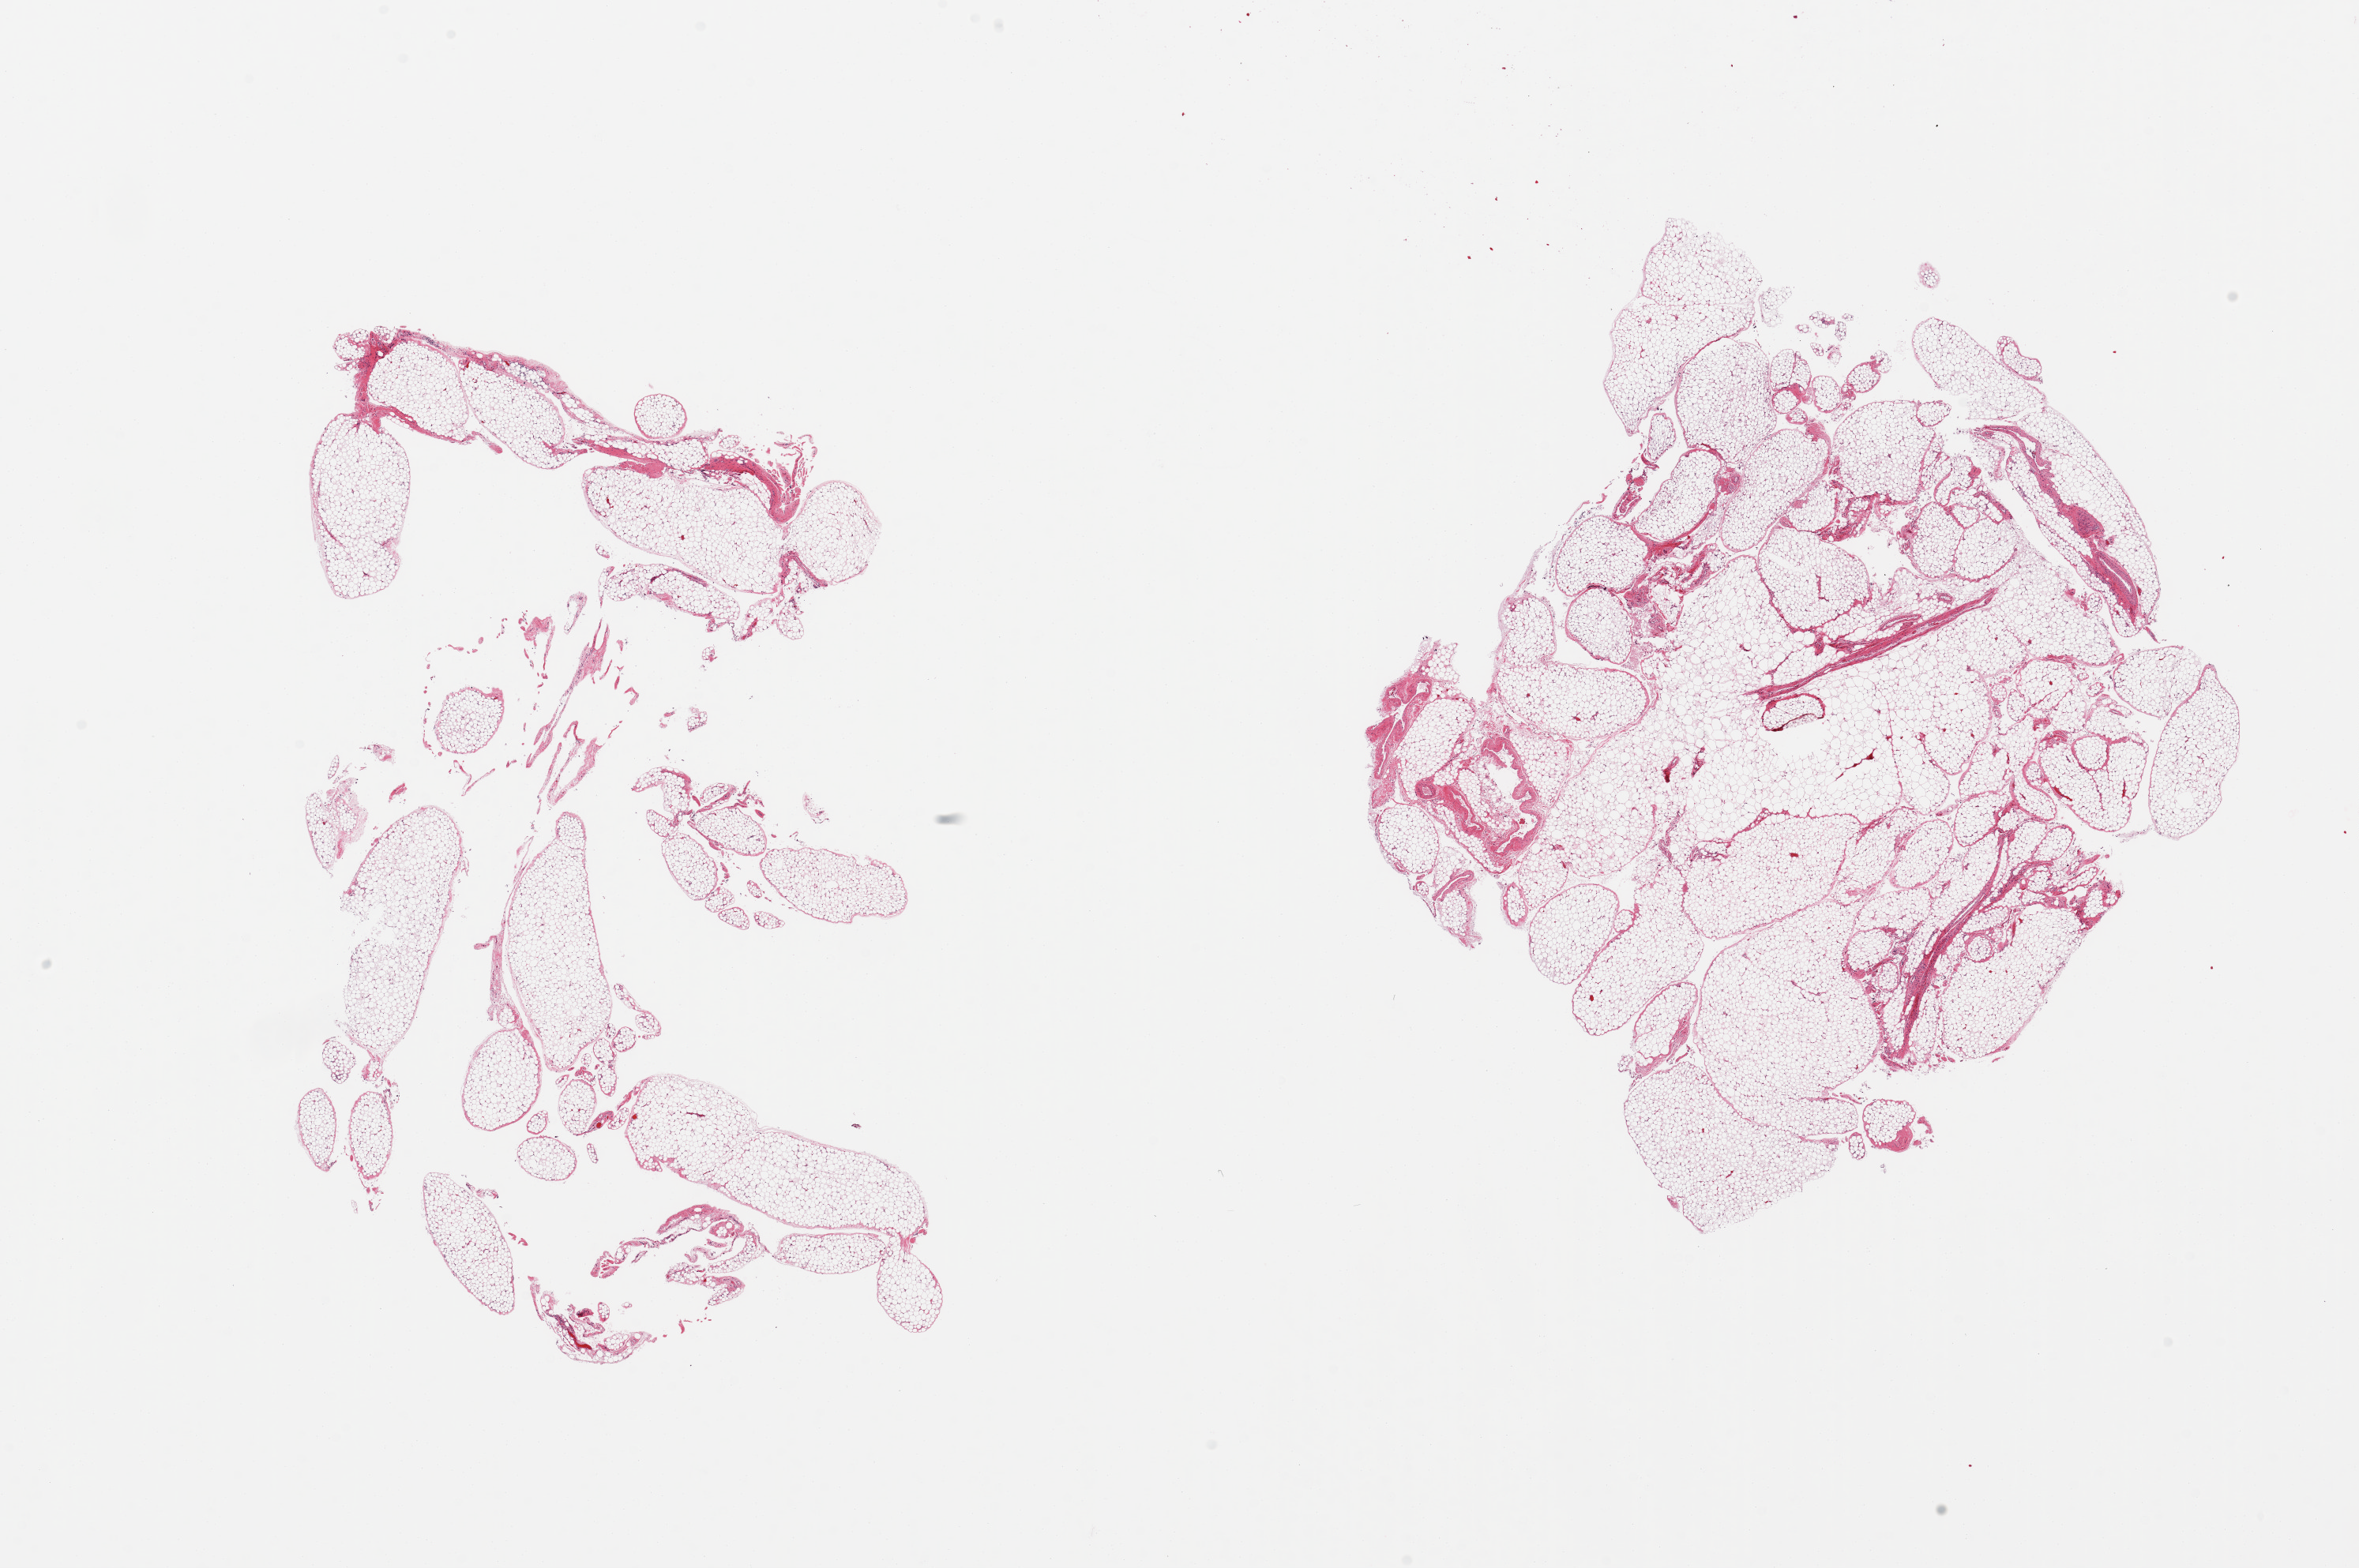
Digitized haematoxylin and eosin-stained section, a low-resolution overview of the entire scanned area, about 23.6 x 15.7 mm; PAXgene-fixed paraffin-embedded (PFPE) section; target tissue: omentum; tissue donor sample. Donor: male.
Reviewer comment on this tissue sample: 2 pieces; 5% fibrous content.